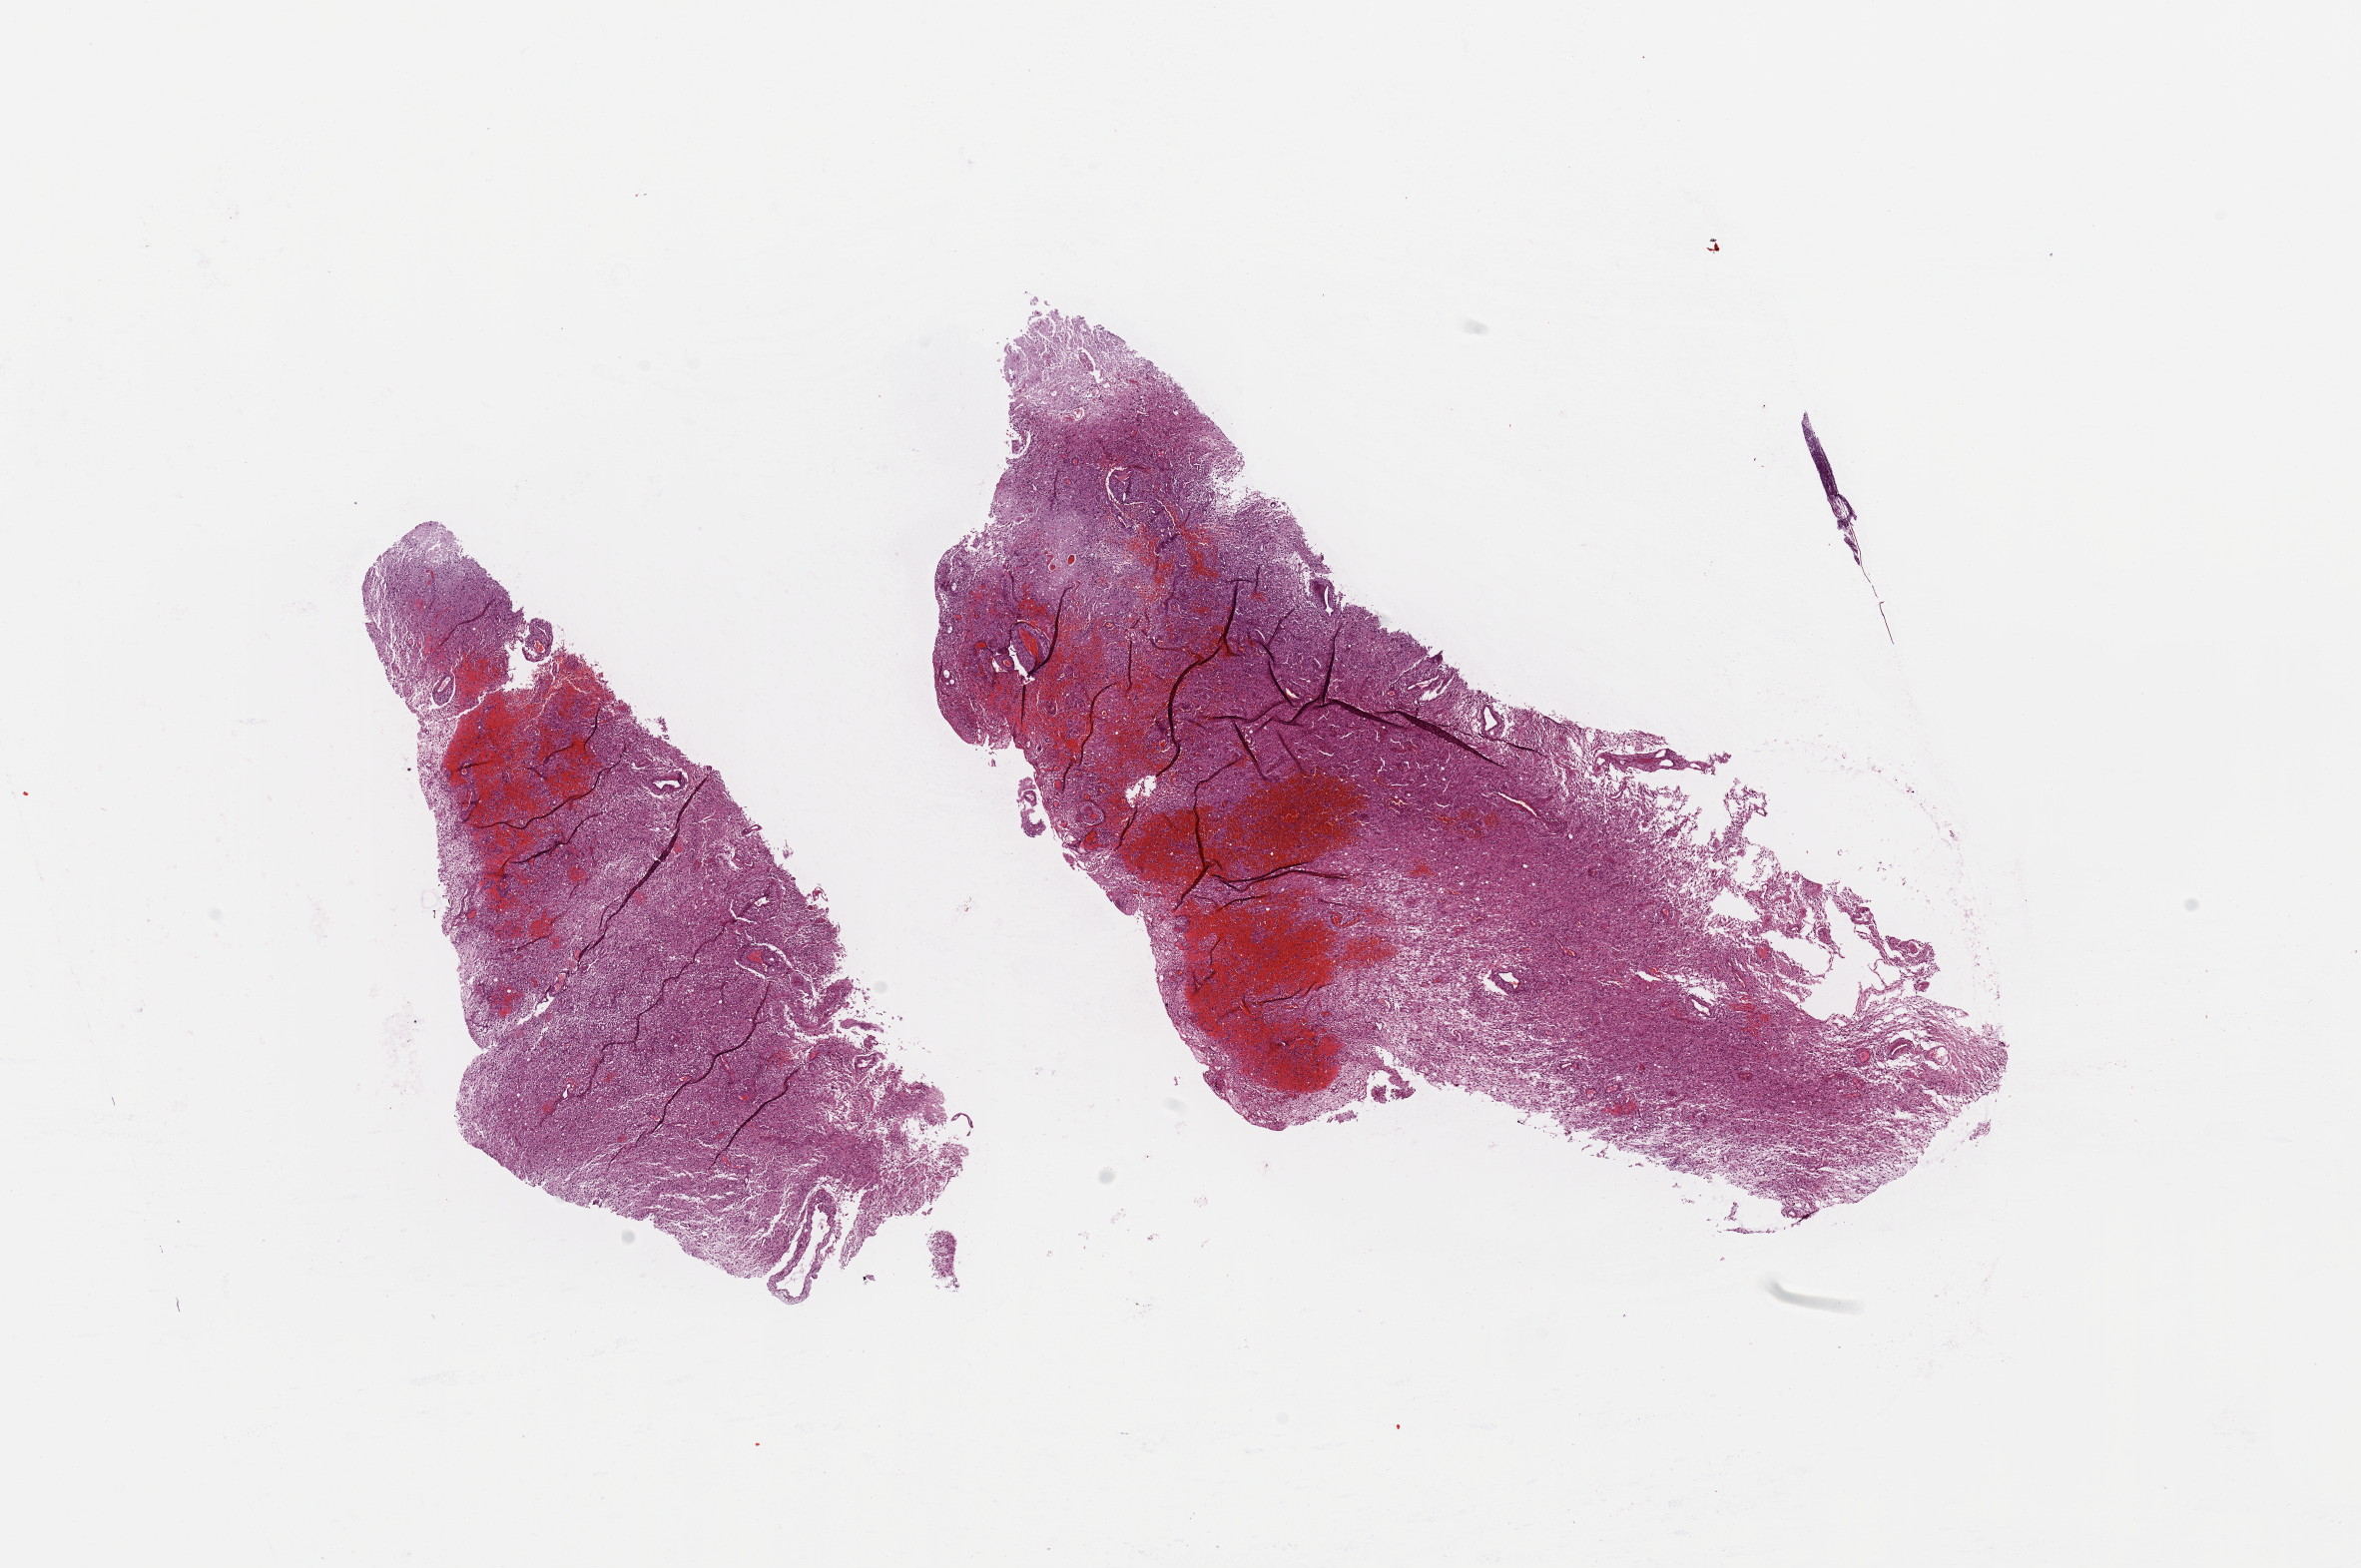
Digitized H&E-stained tissue section (whole slide) — a low-resolution overview of the entire scanned area, about 18.7 x 12.4 mm (acquisition: 20x scan); brain, tumour tissue. Patient: male, age 53 years.
Histologic diagnosis: Glioblastoma. Primary tumour site (as recorded): occipital lobe.